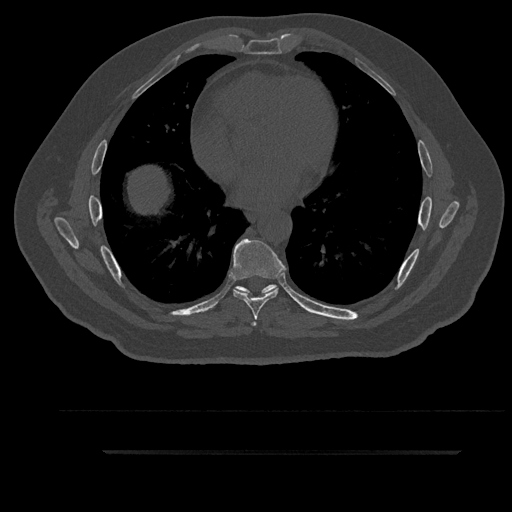
CT including the spine, one axial slice; slice 512 of 797 in the series (ordered by position); bone window (W 1800 / L 400 HU); 0.5 mm slice thickness; 512 × 512 image matrix. Male patient, age 63 years. From the clinical record (not read from this slice): primary cancer: renal; vertebrae with lytic lesions (as recorded): T8.
Outlined on this slice (semi-automatically segmented with operator editing):
- T6 vertebra: bounding box [x1, y1, x2, y2] px = [235, 288, 270, 326]
- T7 vertebra: [232, 238, 286, 320]
- T8 vertebra: [235, 284, 278, 293]